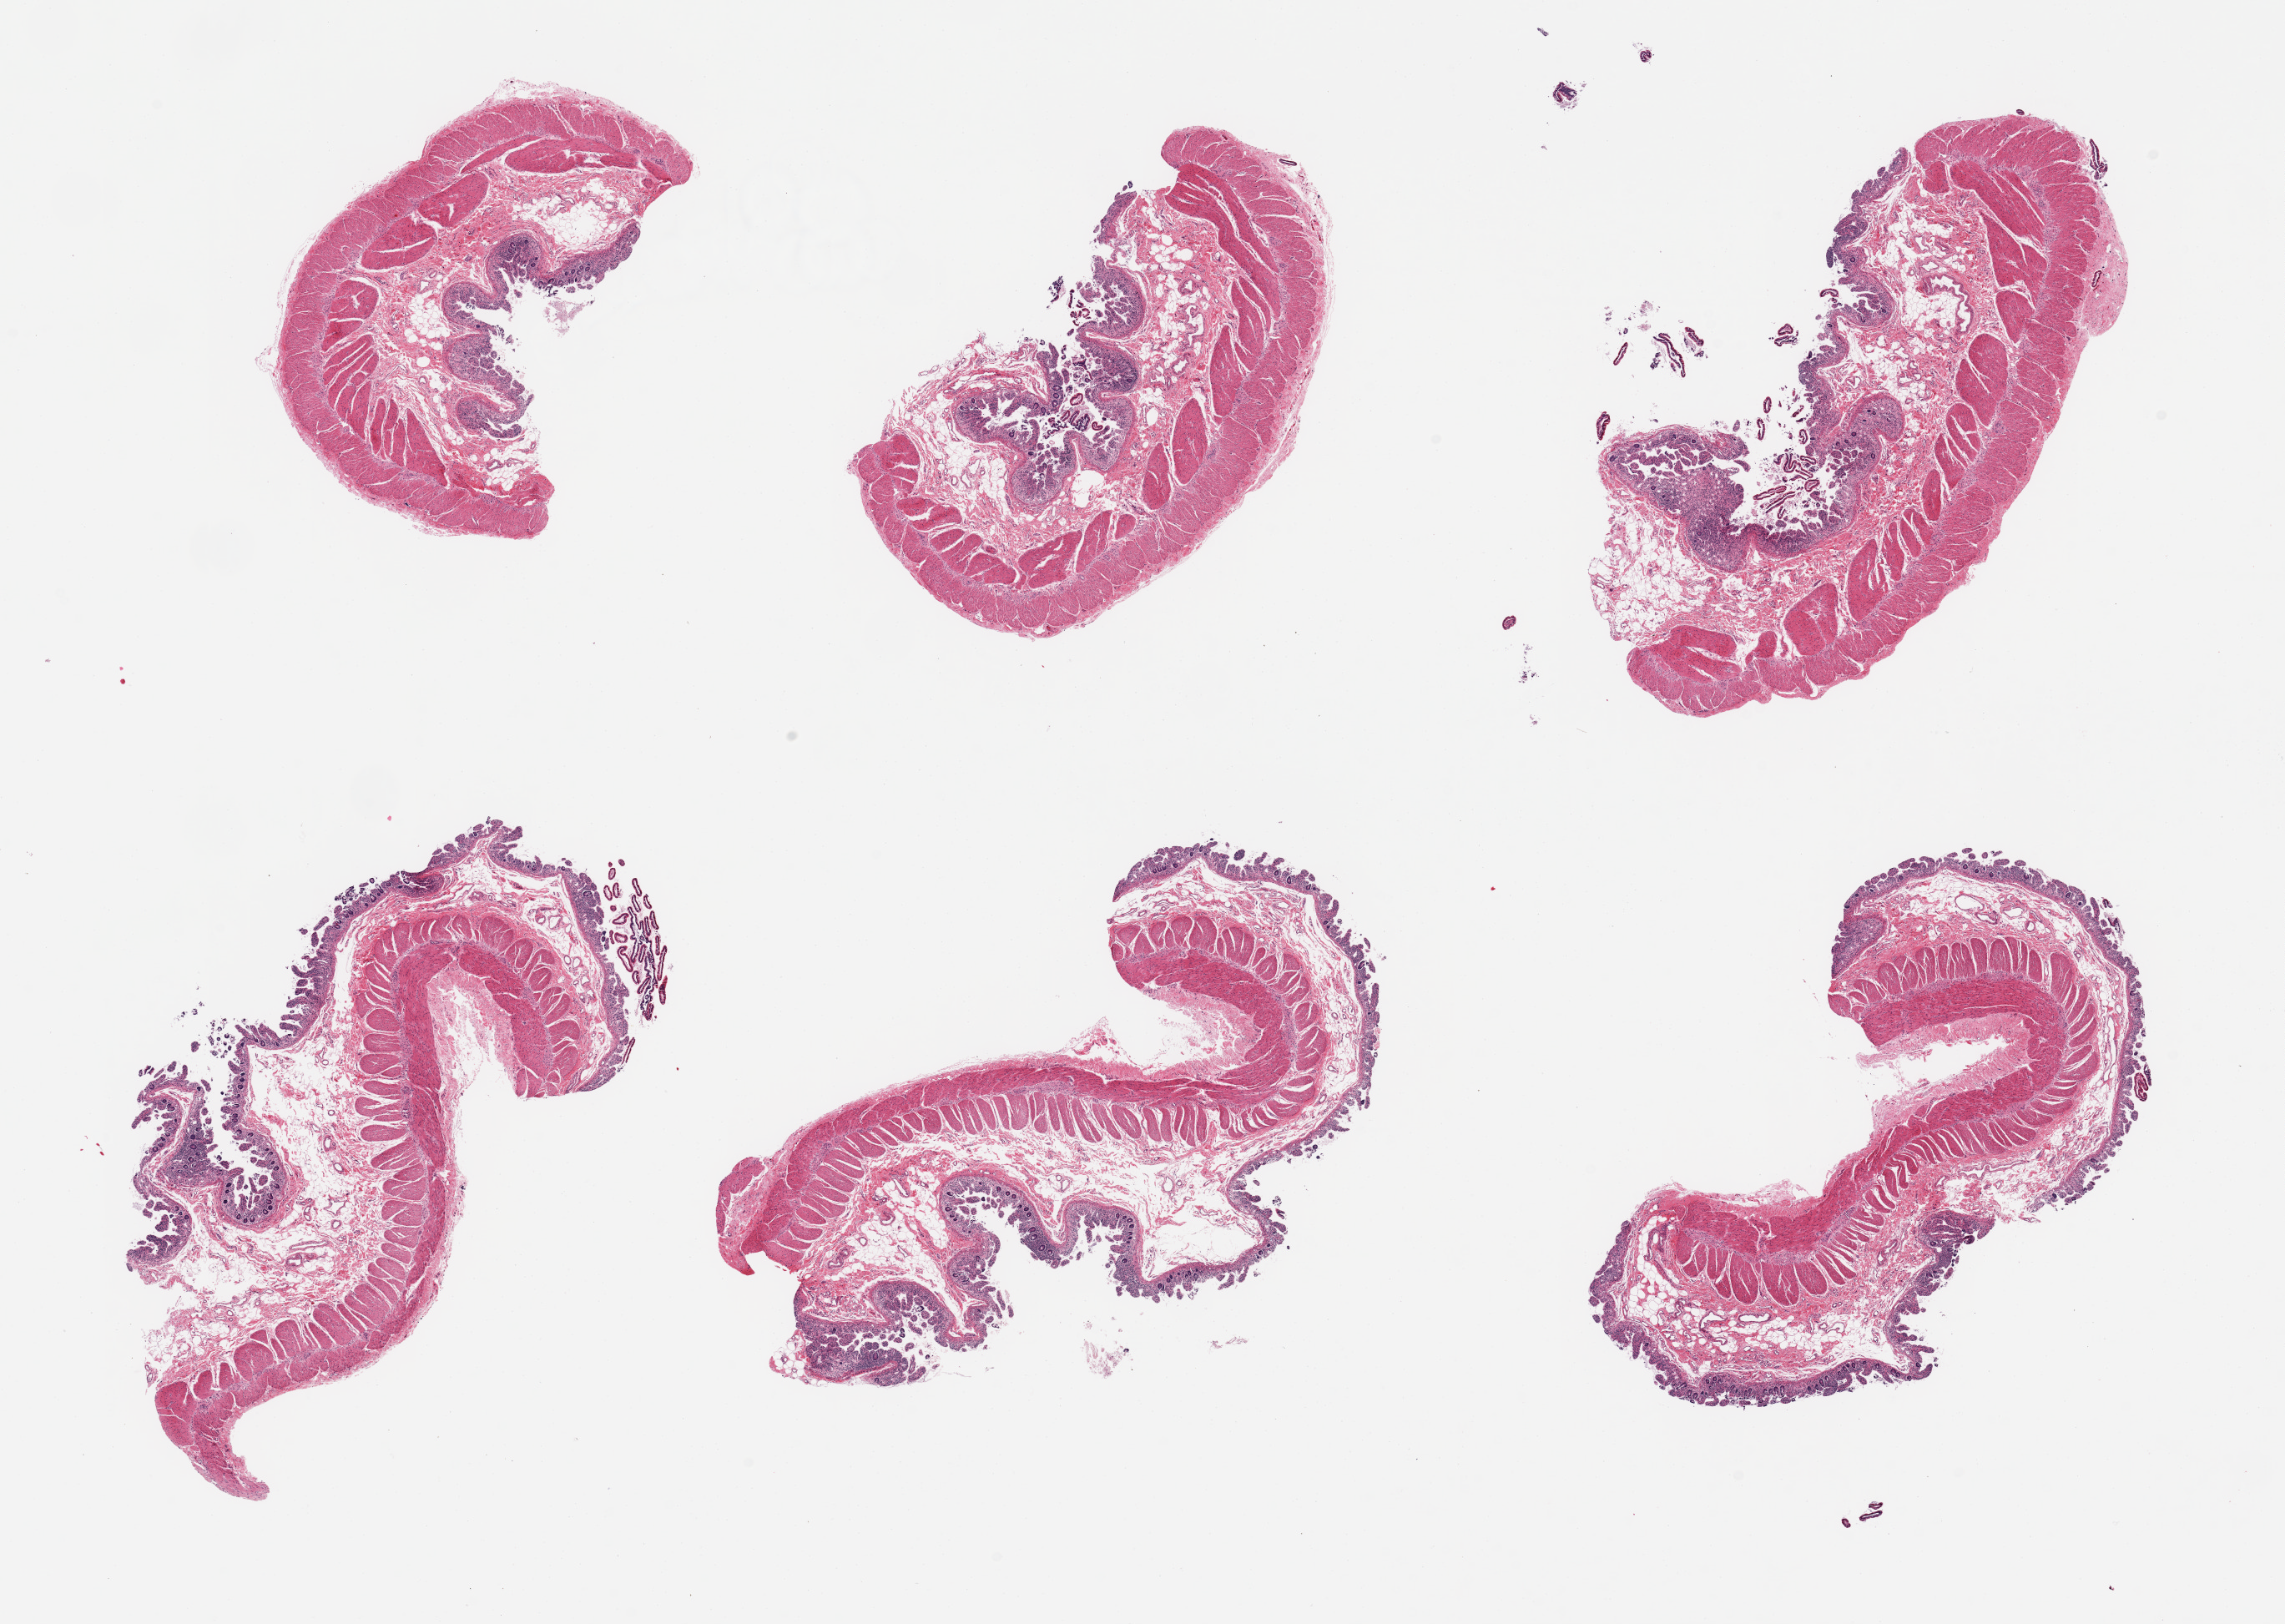
Digitized H&E-stained section, brightfield, whole scanned area (about 21.7 x 15.4 mm) shown as a low-resolution overview, PAXgene-fixed, paraffin-embedded tissue, sampled site (target tissue): ileum, tissue donor sample.
• review note (as recorded): 6 pieces; full thickness ileum with no lymphoid deposits